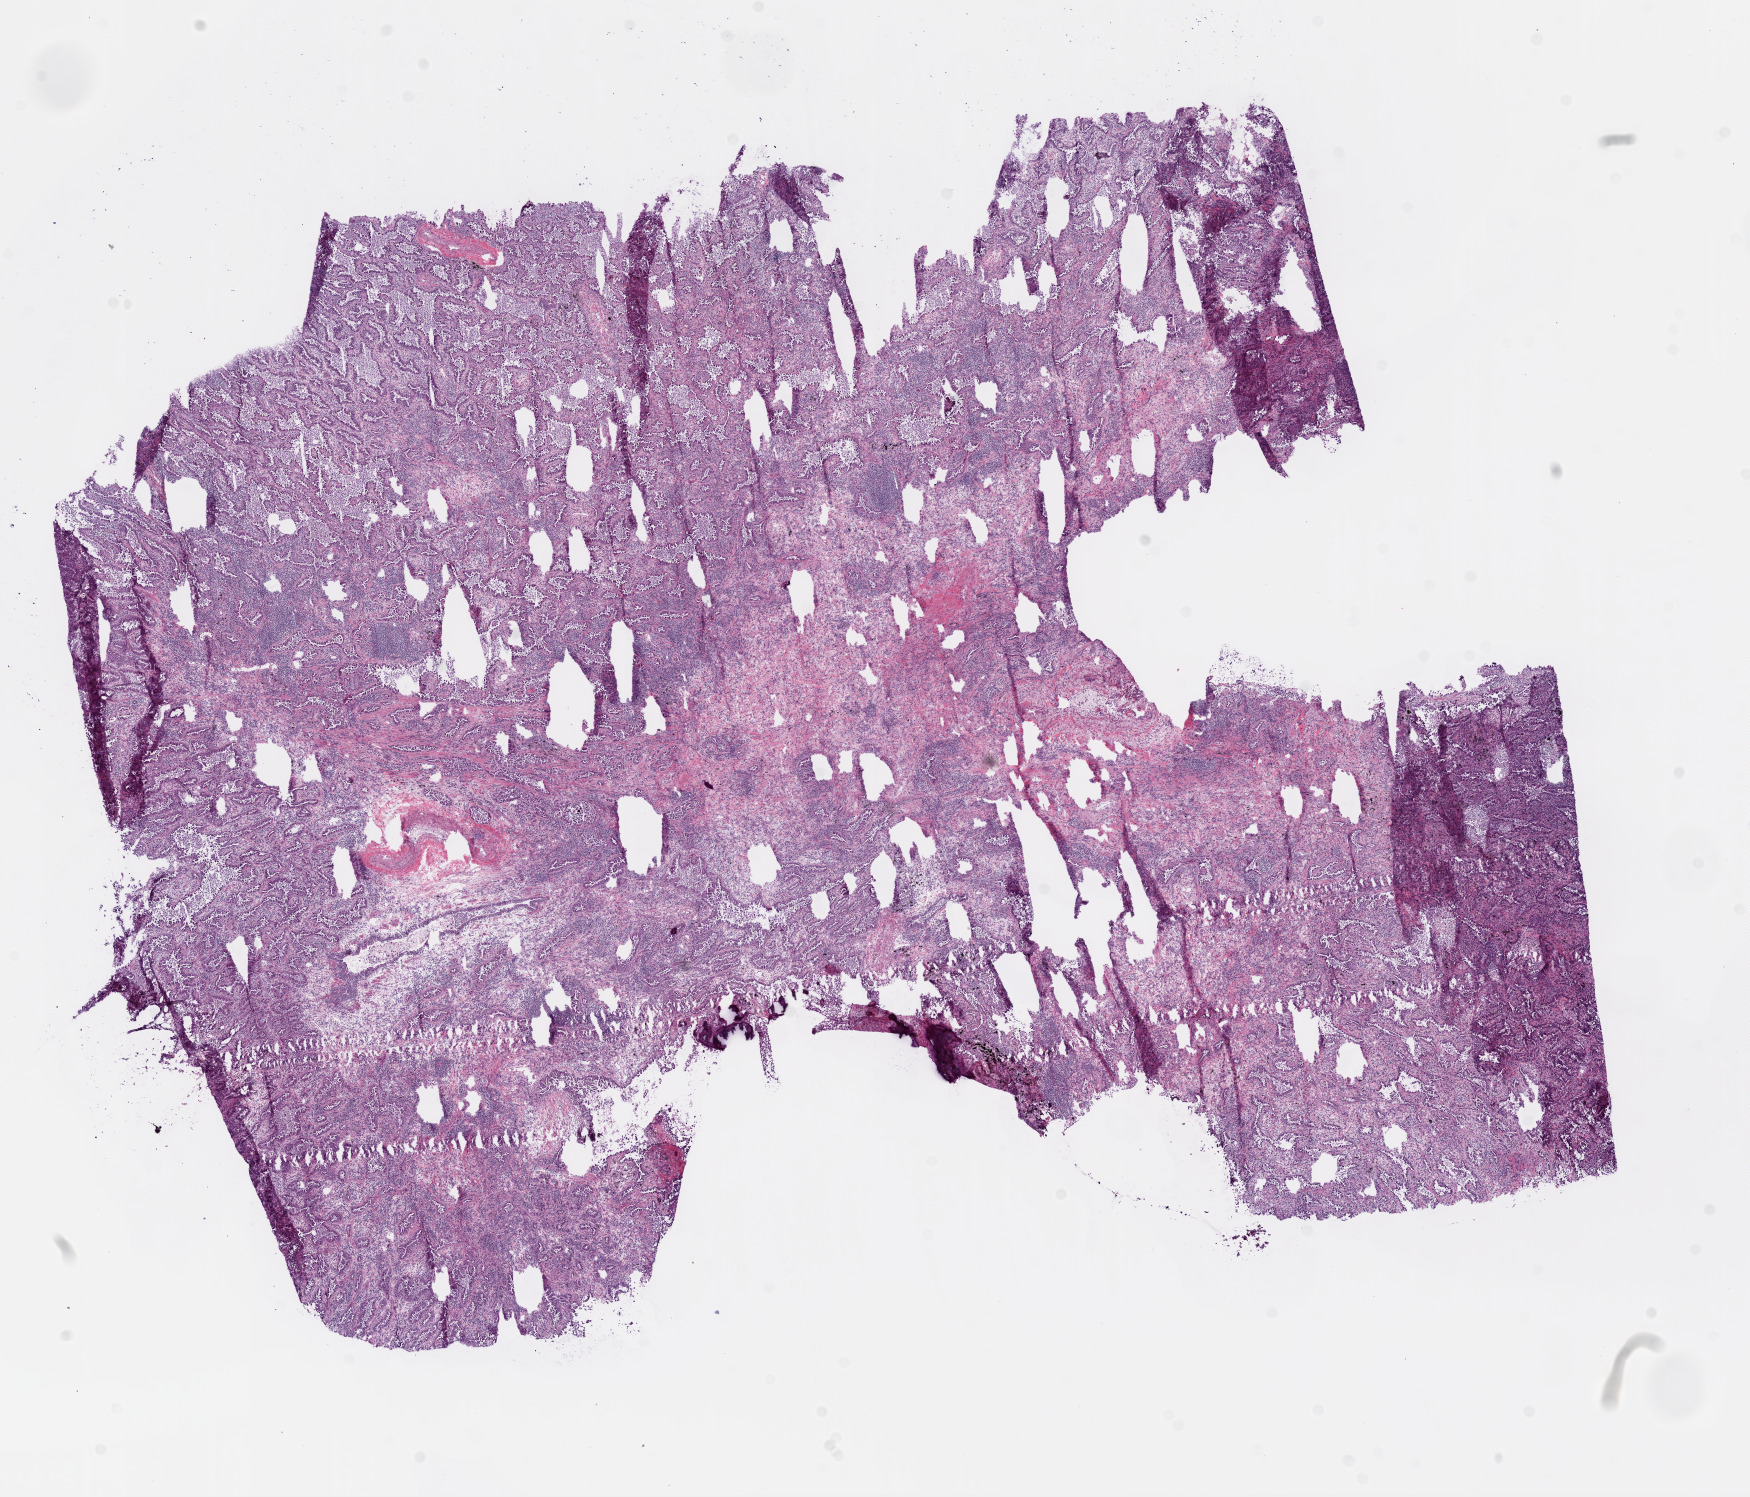
Whole-slide histology image, H&E, whole scanned area (about 14.0 x 12.0 mm, from a 20x scan) shown as a low-resolution overview, frozen section from the bottom of the tissue portion, primary tumour sample from the lung. Patient: female, age at initial diagnosis 69 years. Pathologist review of this section (percent, as recorded): tumour cells 90%, tumour nuclei 65%, normal cells 0%, stromal cells 10%, necrosis 0%. Inflammatory infiltration, as recorded: lymphocyte infiltration 15%, monocyte infiltration 5%.
TNM: T1 N0 M0. AJCC pathologic stage: IA (6th edition). Laterality: left. Diagnosis: Adenocarcinoma, NOS (upper lobe, lung).